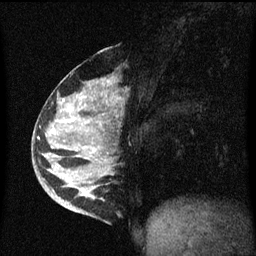
Breast MRI (dynamic contrast-enhanced), one sagittal slice; slice 24 of 60 in the series (ordered by position); dynamic contrast-enhanced series, image 2 of 3 at this slice position (ordered by acquisition); 1.5 T; TE 4.2 ms, TR 8.4 ms; 256 × 256 image matrix. Patient: female, 34 years. Case-level facts recorded for this patient, not image findings: setting: breast cancer imaged before/during neoadjuvant chemotherapy; receptor status: HR-positive, HER2-negative.
Annotated regions visible in this slice (semi-automatic segmentation, software-assisted and operator-edited):
- analysis volume of interest (the breast-tissue region the enhancement analysis was run in; not a lesion): bounding box <34,48,119,215> (left, top, right, bottom; pixels)
- tumour enhancement mask (voxels above the 70 % enhancement threshold inside the analysis volume of interest): <82,188,91,197>